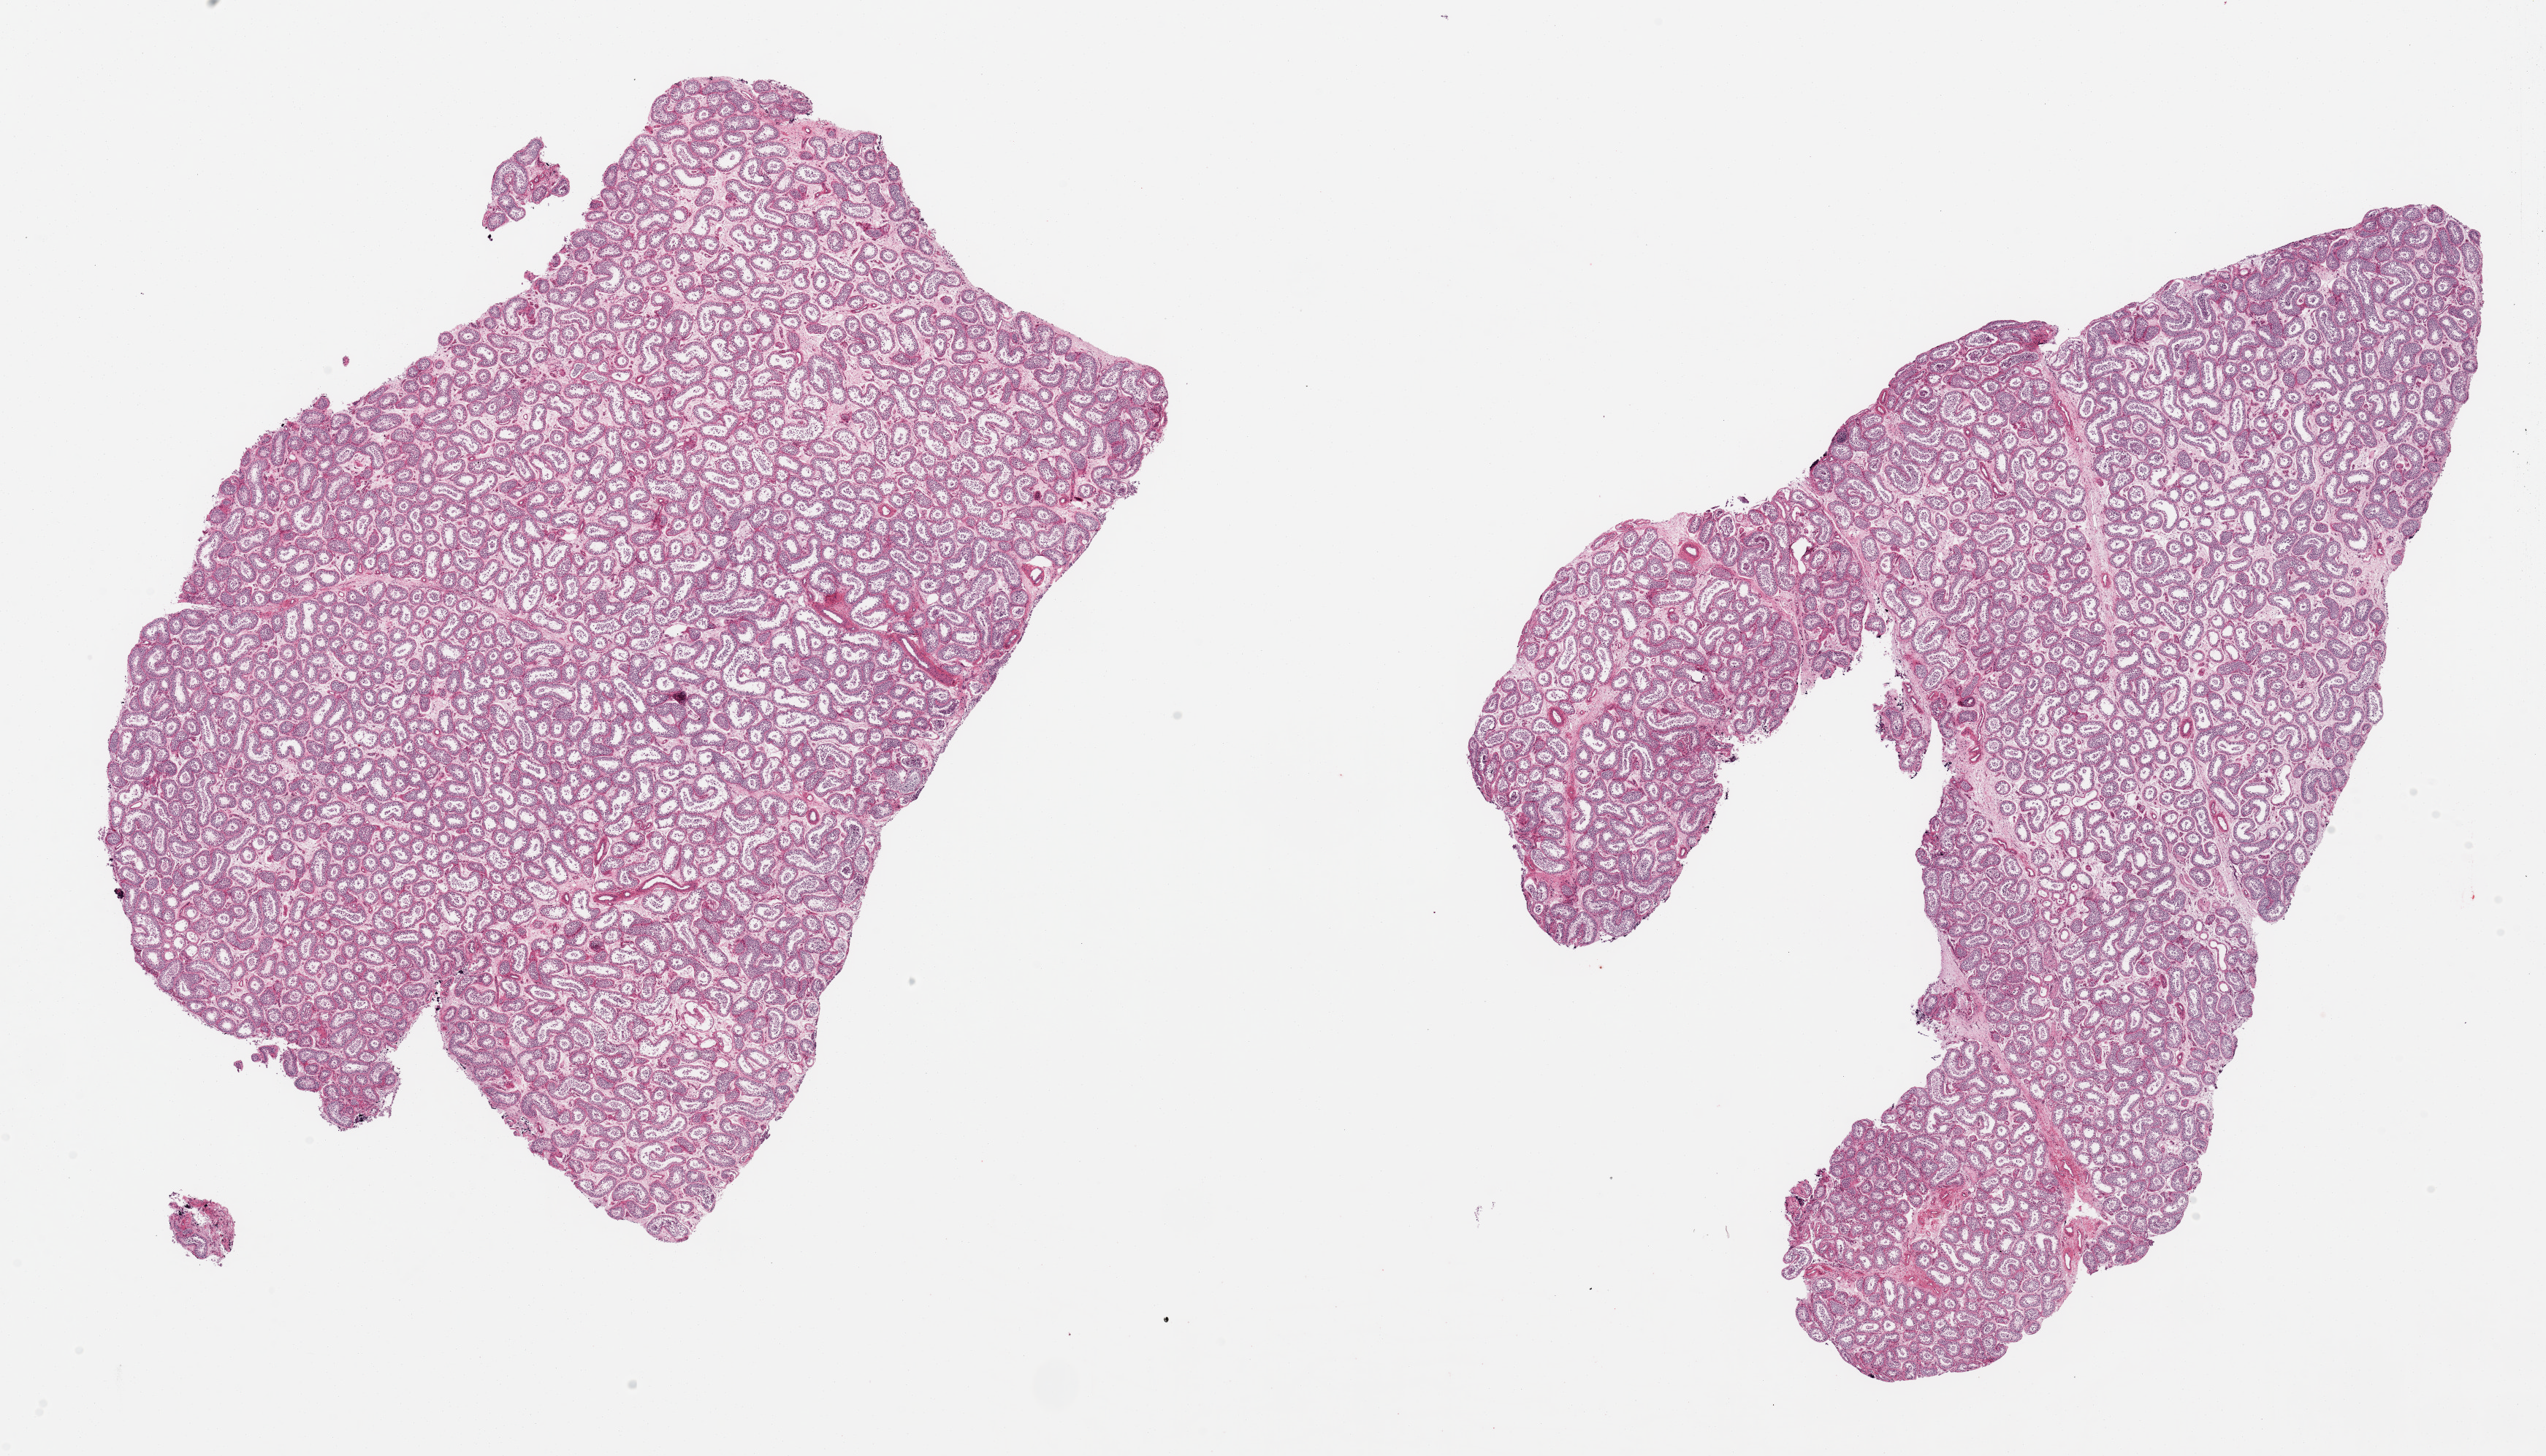
Haematoxylin and eosin whole-slide image — a low-resolution overview of the entire scanned area, about 27.6 x 15.8 mm (acquisition: 20x scan). PAXgene-fixed paraffin-embedded (PFPE) section. Sampled site (target tissue): testis. Tissue donor sample. Donor: male.
Review note (as recorded): 2 aliquots, ~12x7mm. Spermatogenesis appears markedly reduced.